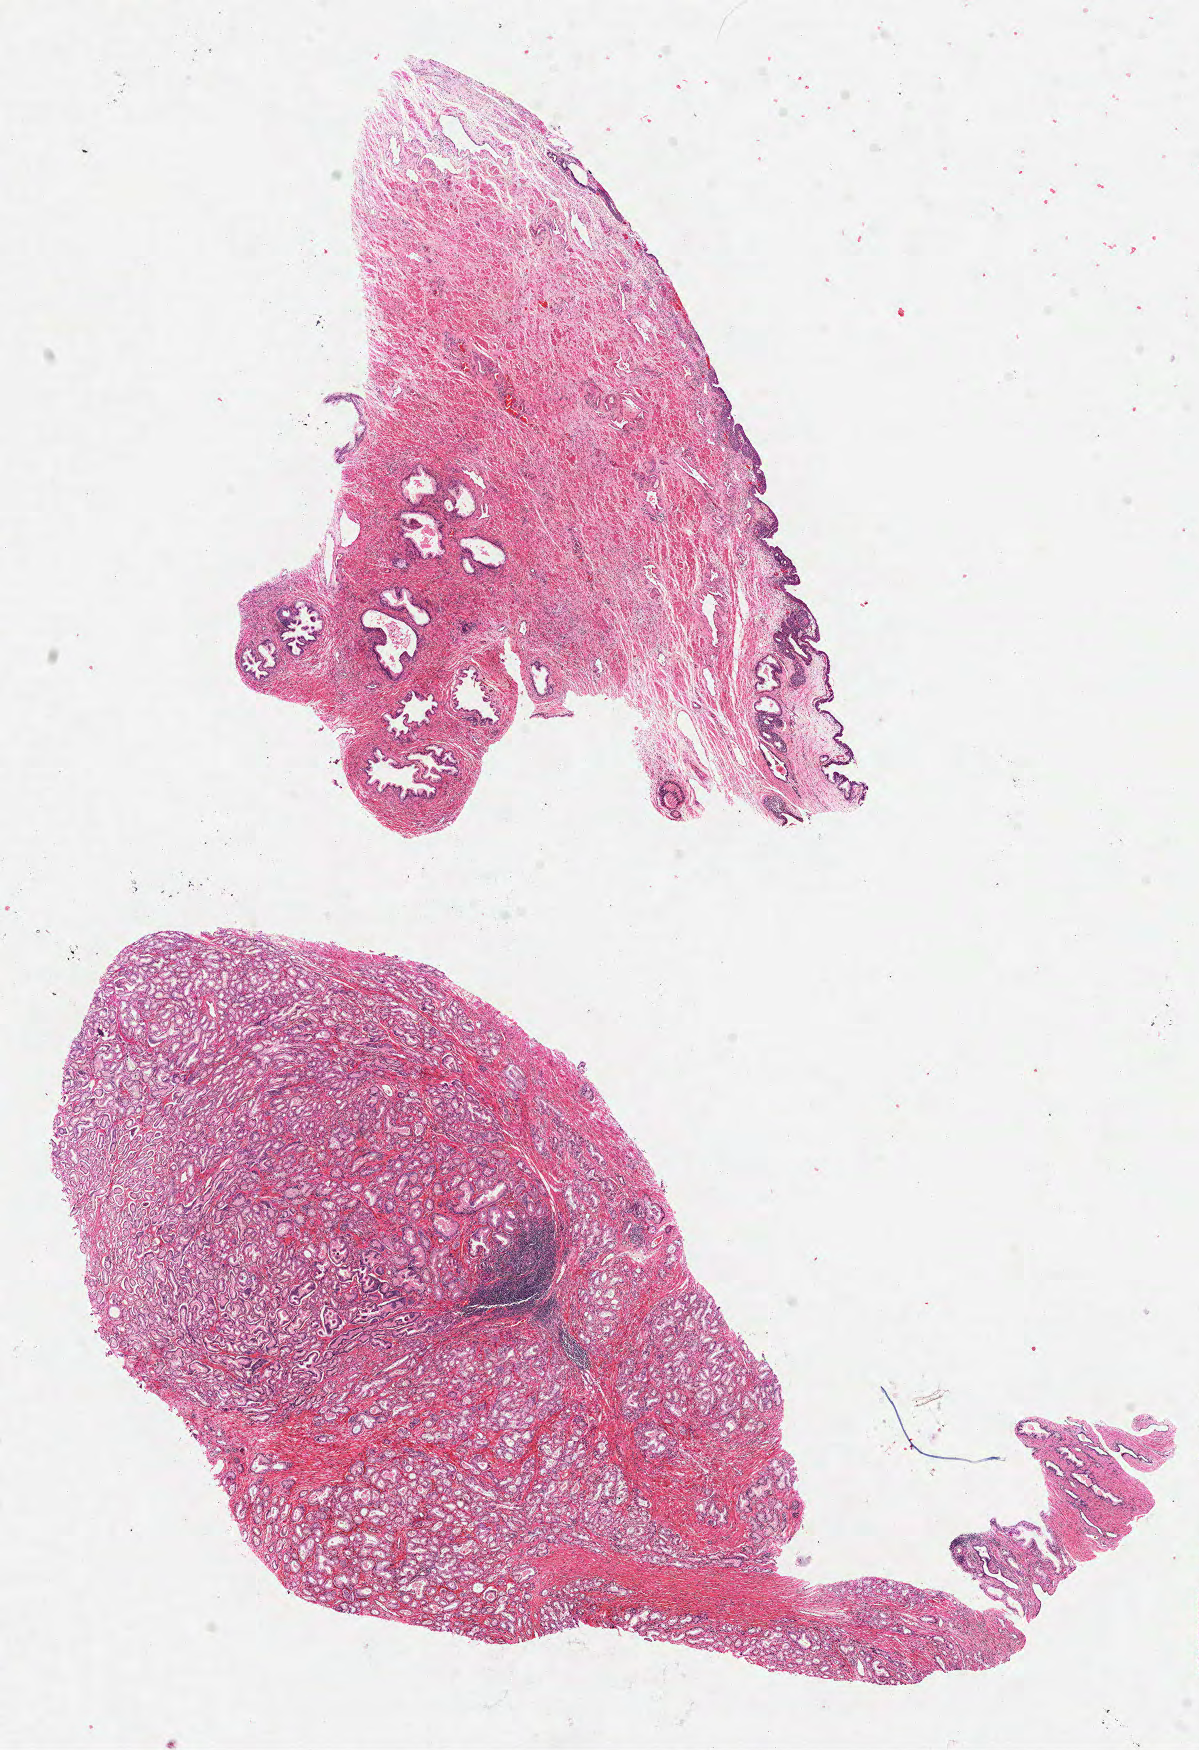
Hematoxylin and eosin (H&E) stained whole-slide image — a low-resolution overview of the entire scanned area, about 9.7 x 14.1 mm (from a 40x scan). FFPE section. Sample: primary tumour, prostate. Male, age 58 years at initial diagnosis. Gleason score: 6 (3+3).
- laterality: bilateral
- histologic diagnosis: Acinar cell carcinoma (prostate gland)